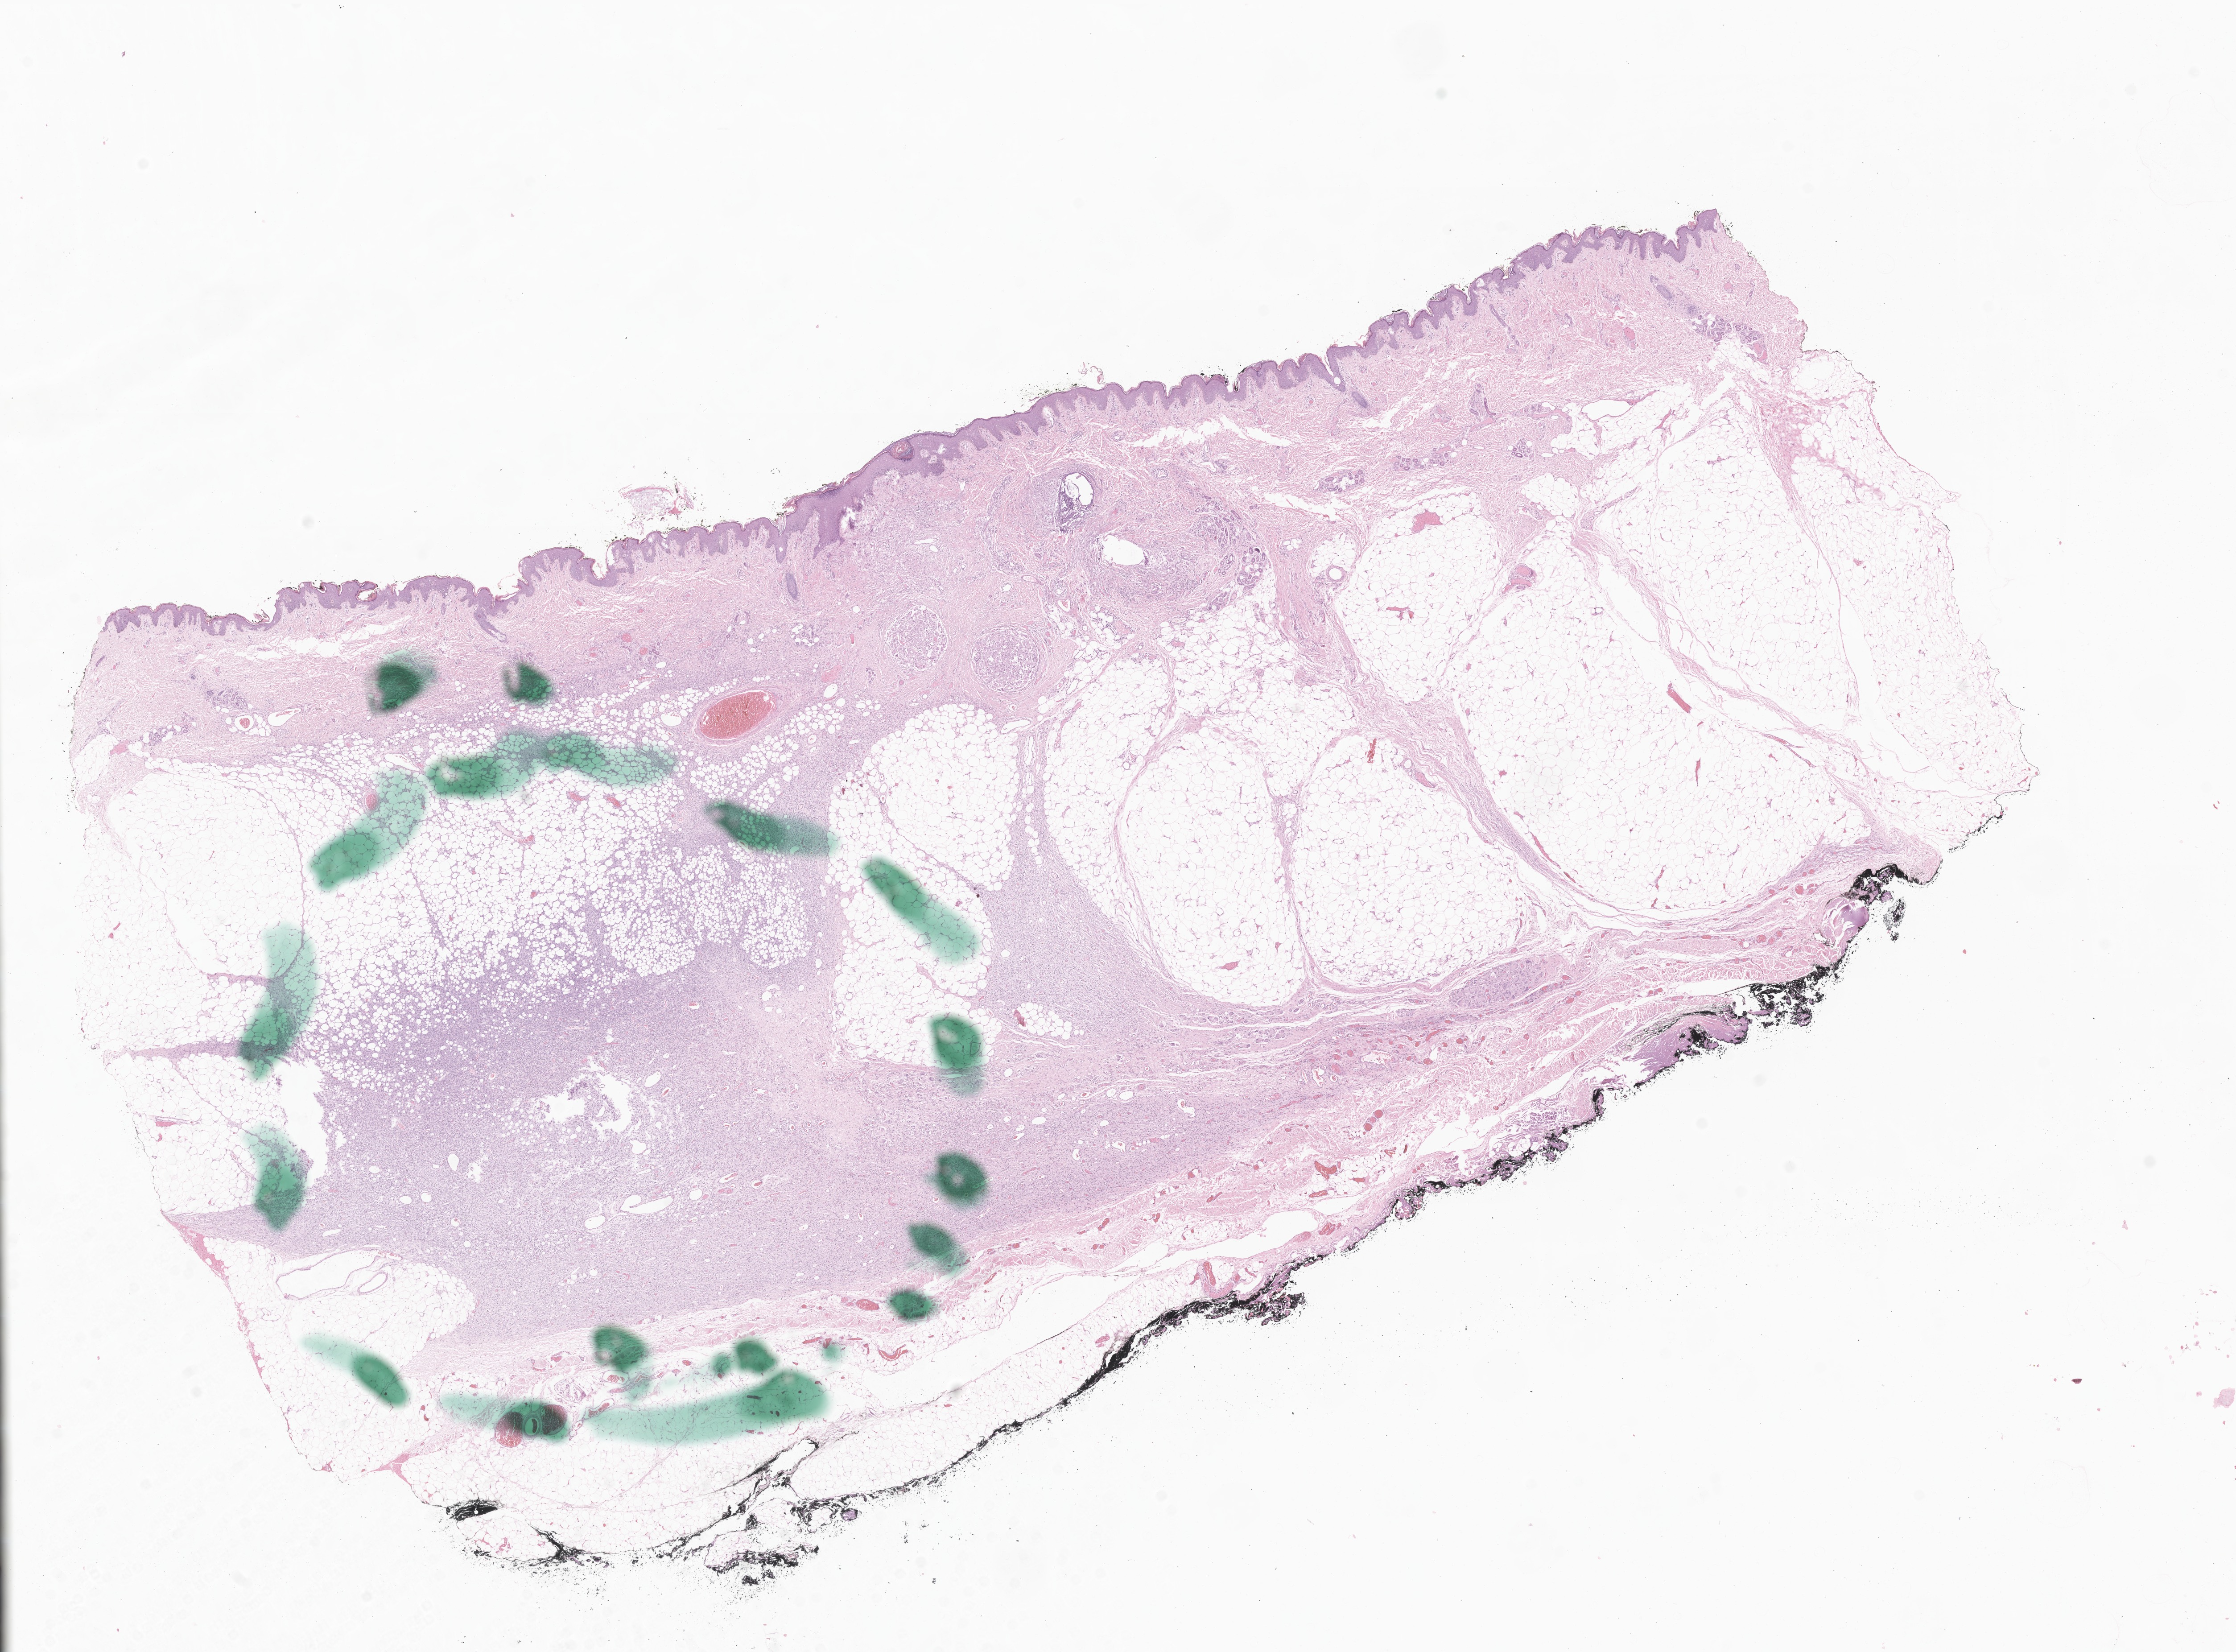
Hematoxylin and eosin (H&E) whole-slide image of tumor tissue from the soft tissue of lower extremity — low-resolution overview of the scanned area, about 21.1 x 15.6 mm, FFPE section. Male patient, age 933 days (about 2.6 years).
Tissue or organ of origin (case record): connective, subcutaneous and other soft tissues of lower limb and hip. Recorded diagnosis: Pigmented dermatofibrosarcoma protuberans.